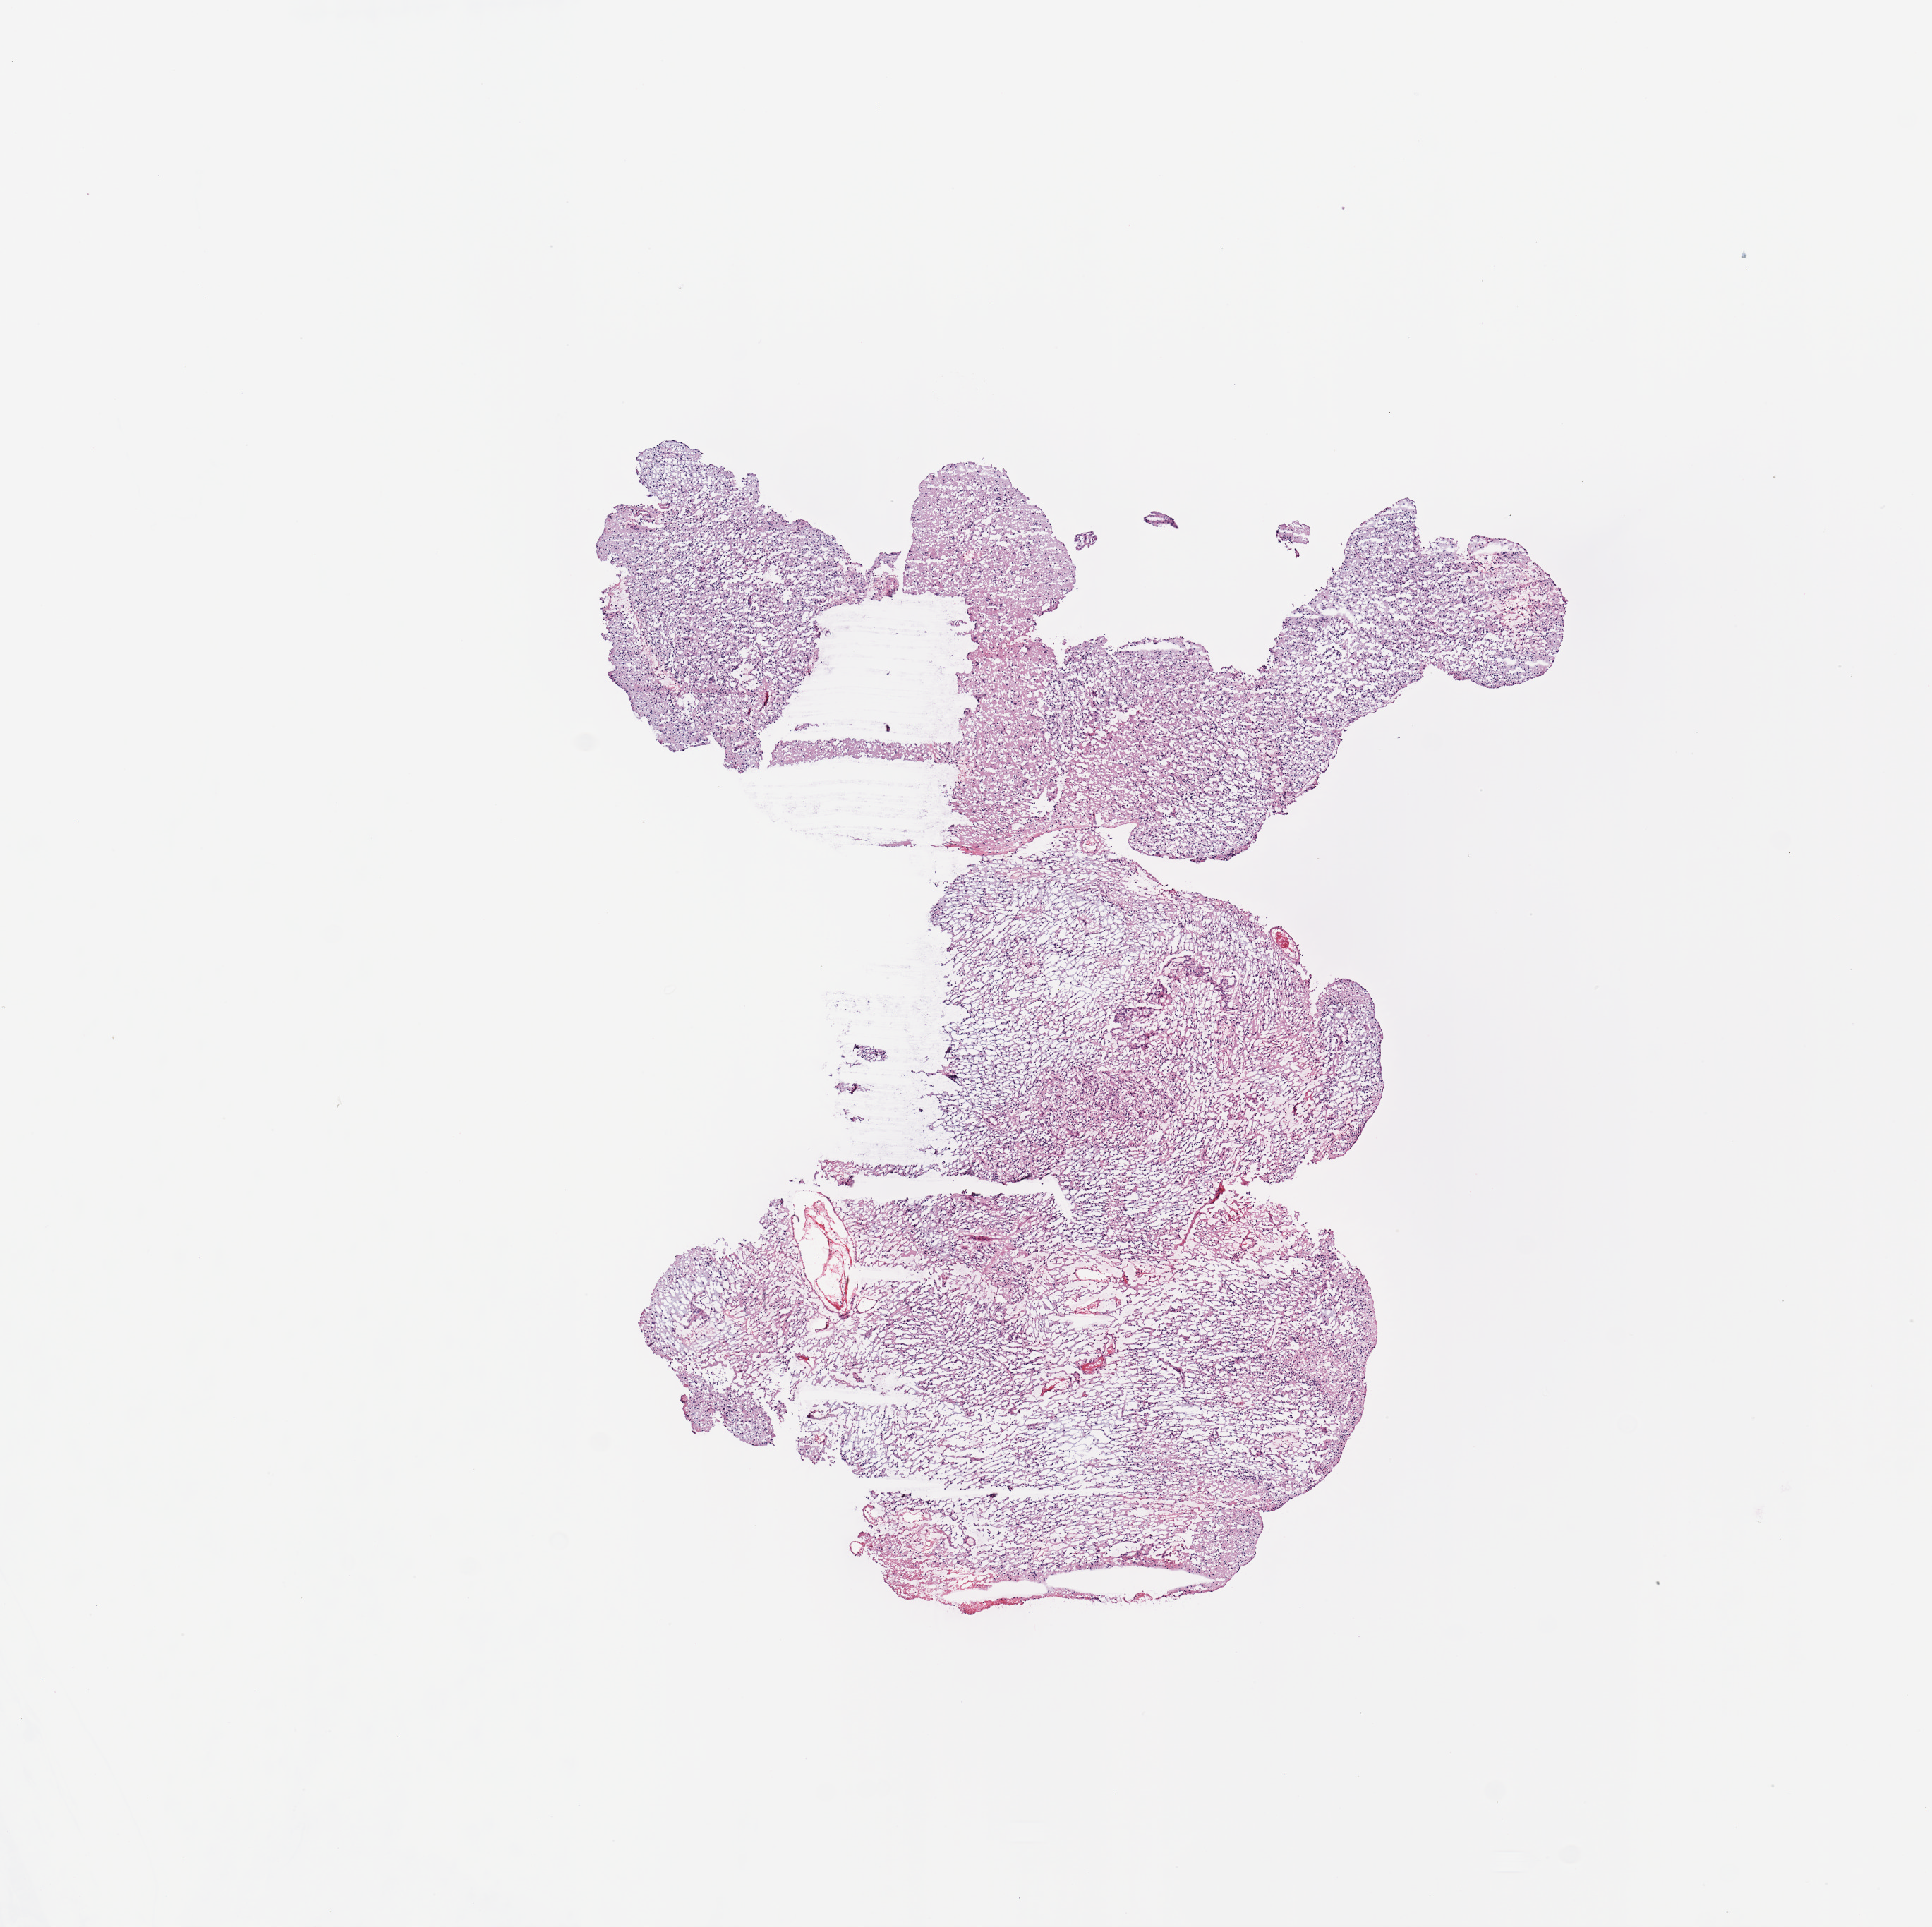
Digitized H&E-stained tissue section (whole slide) — whole scanned area (about 10.8 x 10.8 mm) shown as a low-resolution overview; tumour tissue sample, brain. 82-year-old male patient.
Primary tumour site (as recorded): temporal lobe. Patient diagnosis (cohort enrolment): glioblastoma multiforme (brain).